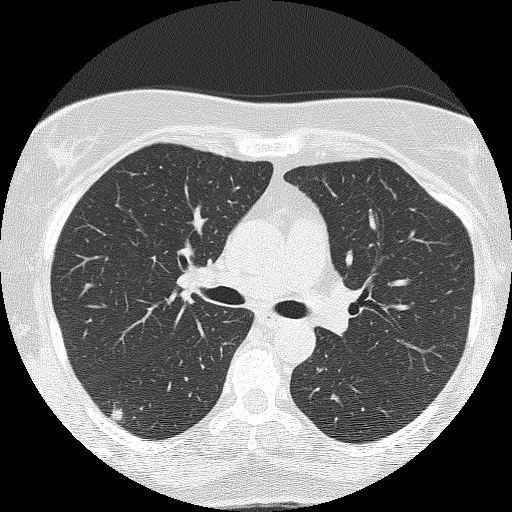
Axial slice from a low-dose chest CT screening exam. Second annual screen. Lung window (W 1500 / L -600 HU). Lung (sharp) reconstruction kernel (FC51). 512 × 512 image matrix. Female, age 58 years at enrolment.
Lesion marked by an expert reader, box from (x=93, y=394) to (x=141, y=430) px. The screening reader recorded 2 non-calcified nodules or masses ≥4 mm on this exam (right upper lobe, right upper lobe); which of them this box marks is not recorded. Later outcome: lung cancer diagnosed 264 days after this screen — adenocarcinoma, NOS, right lower lobe, well differentiated (G1), stage IB (AJCC 6th edition), 10 mm at pathology.